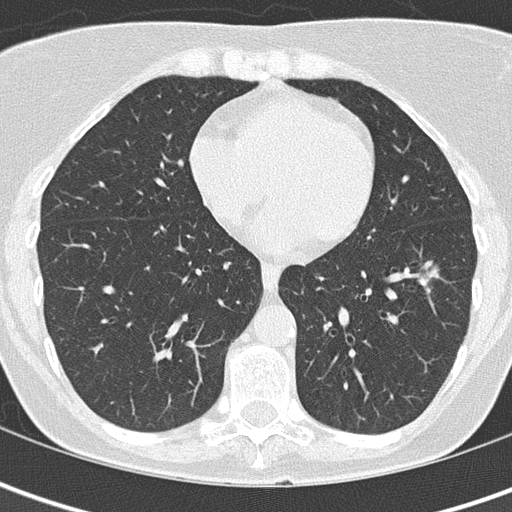
Chest CT (low-dose screening protocol), one axial image; first (baseline) screen; lung window (W 1500 / L -600 HU); 512 × 512 image matrix. Female participant, aged 61 years at enrolment.
Expert reader's lesion annotation, bounding box (x1, y1, x2, y2) in pixels: (379, 248, 453, 304). The exam's reader record, not a measurement of the box and not confirmed to be the same lesion: non-calcified nodule or mass ≥4 mm, left lower lobe, 29 × 16 mm, ground glass attenuation. Official screen result: positive, change unspecified: nodule(s) >= 4 mm or enlarging nodule(s), mass(es), or other non-specific abnormalities suspicious for lung cancer. Lung cancer was diagnosed 259 days after this screen: bronchiolo-alveolar adenocarcinoma, NOS, left lower lobe, well differentiated (G1), stage IA (AJCC 6th edition), 10 mm at pathology.